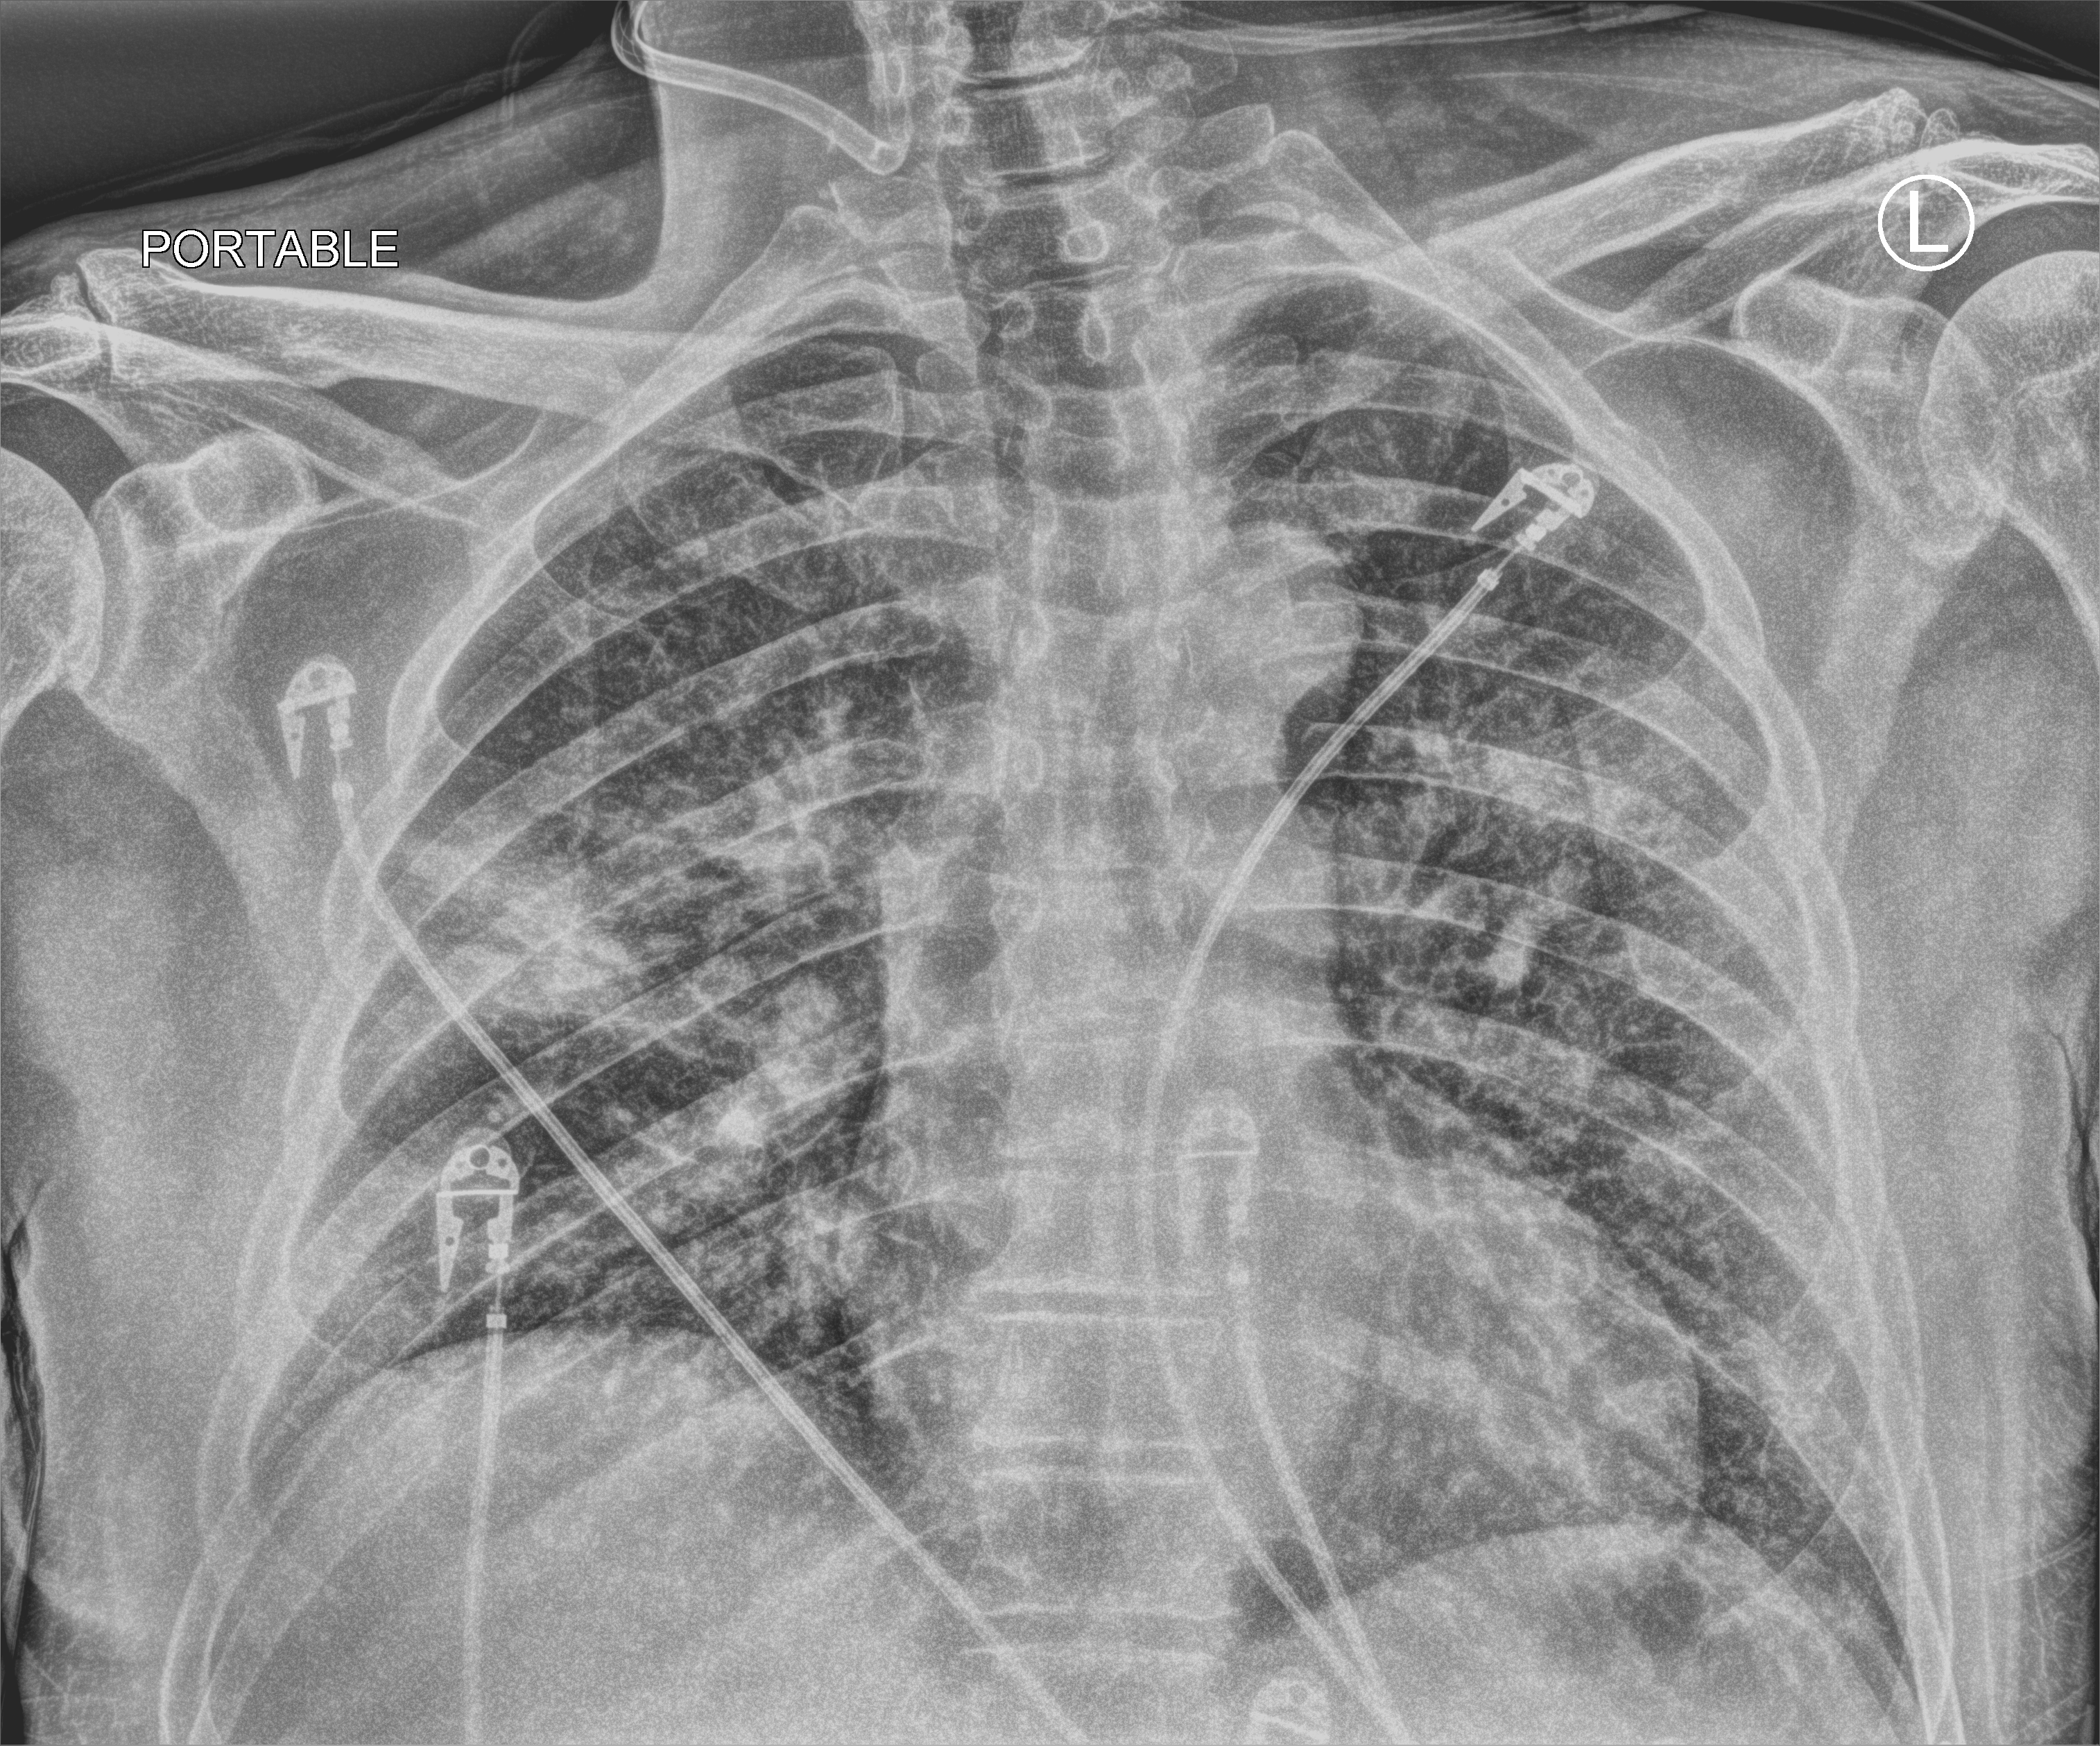
Portable chest radiograph, anteroposterior (AP) projection. Patient hospitalised with COVID-19; male, aged 18–59 years.
From the hospital-stay record, not from the radiograph (when in the stay this image was taken is not recorded): mechanically ventilated during this hospital stay: no.